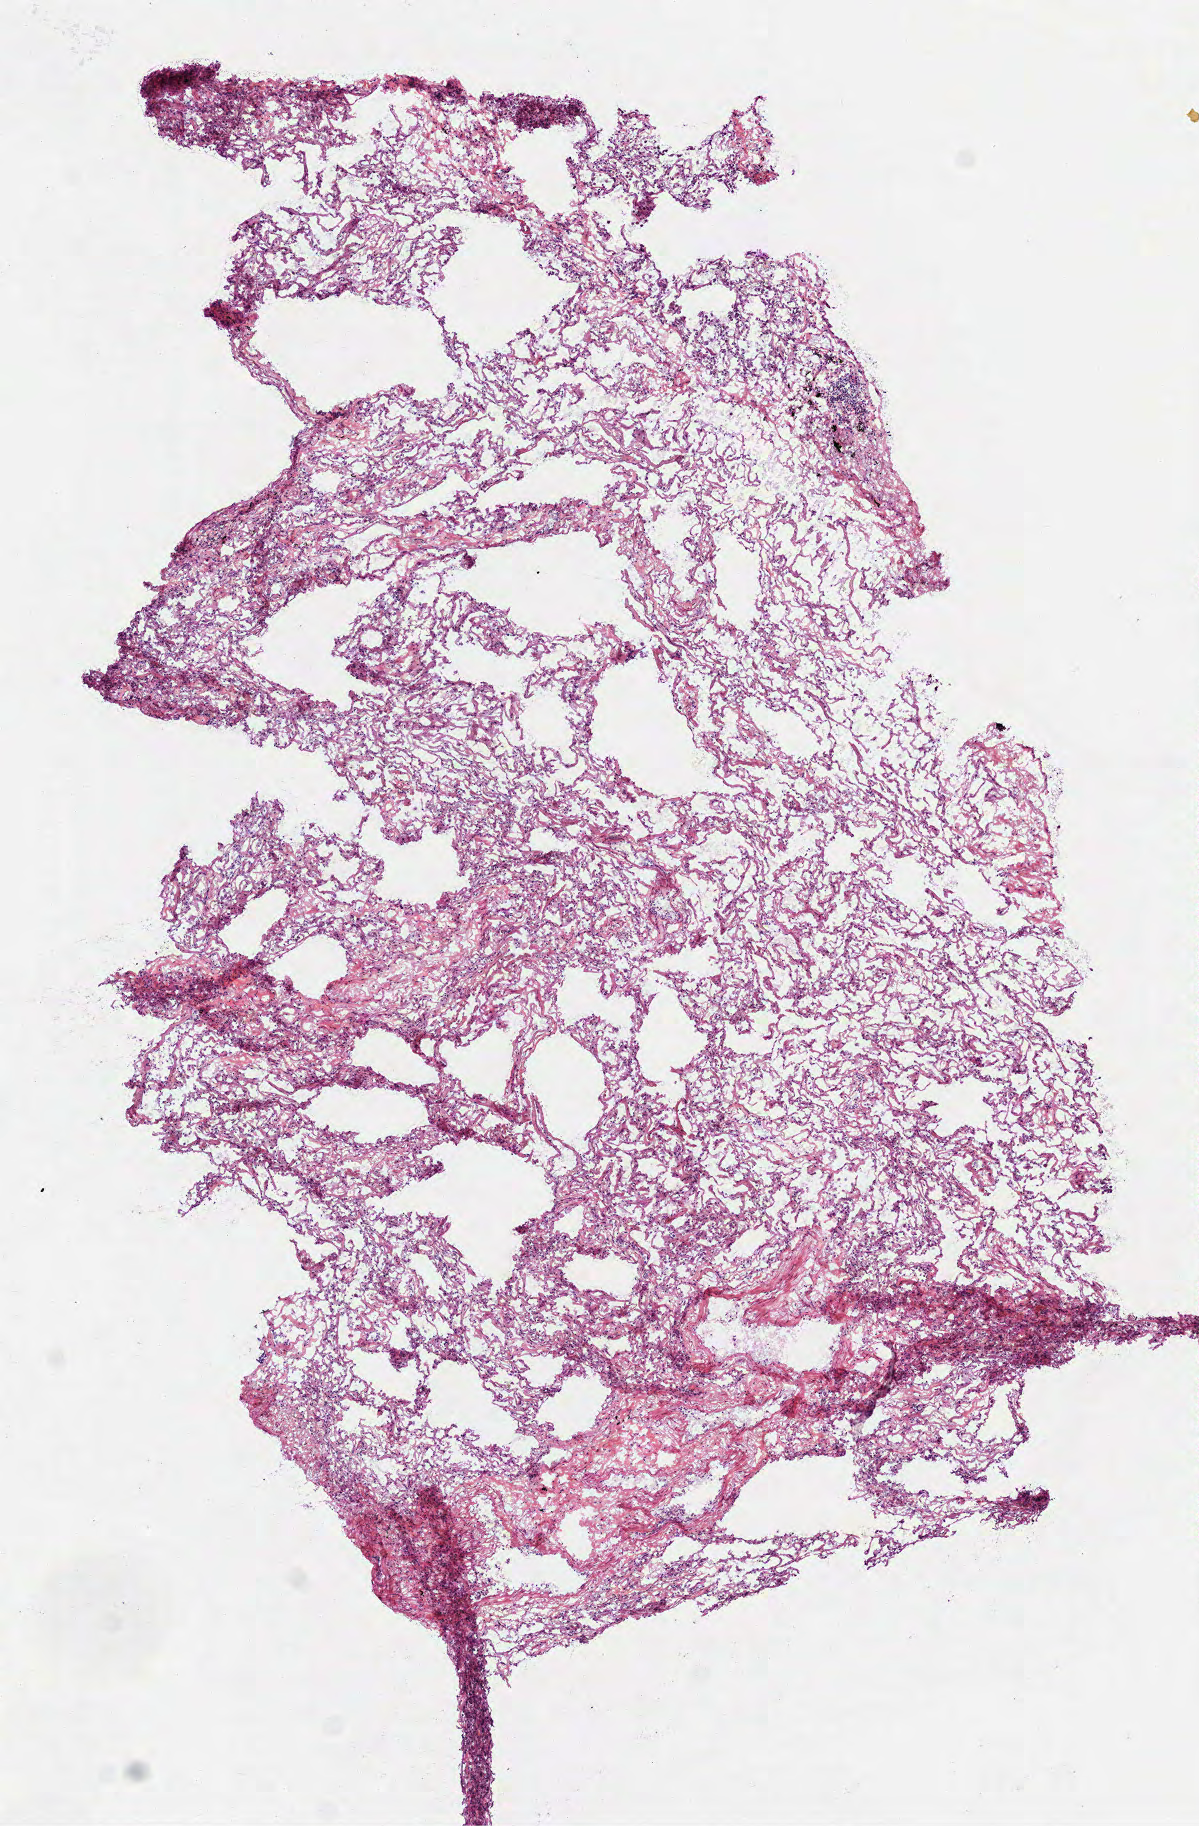
H&E-stained whole-slide image, a low-resolution overview of the entire scanned area, about 4.8 x 7.4 mm (acquisition: 40x scan); frozen section from the top of the tissue portion; sample: solid tissue normal (non-tumour tissue), lung. Female patient; age at initial diagnosis 70 years.
This section: solid tissue normal (non-tumour) sample from the same patient. Patient diagnosis: Adenocarcinoma, NOS (middle lobe, lung).